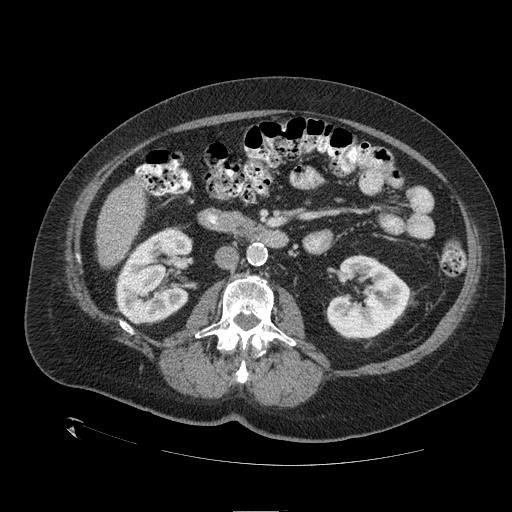
Contrast-enhanced abdominal CT (liver protocol), one axial slice; position 38 of 109 along the scan axis; reconstruction kernel STANDARD; one of 2 acquisitions stored at this slice position; soft-tissue window (W 400 / L 40 HU); 512 × 512 image matrix, field of view 460 × 460 mm. From the clinical record (not read from this slice): diagnosis: hepatocellular carcinoma (patient treated with transarterial chemoembolisation; whether this scan precedes or follows treatment is not stated here); TNM stage (as recorded): Stage-I; Child-Pugh class: A; tumour nodularity: uninodular.
Outlined on this slice (semi-automatically segmented with operator editing):
- liver parenchyma outside the tumour (the mass and vessels are separate outlines, so this box may not span the whole liver): bounding box [x1, y1, x2, y2] px = [96, 178, 146, 266]